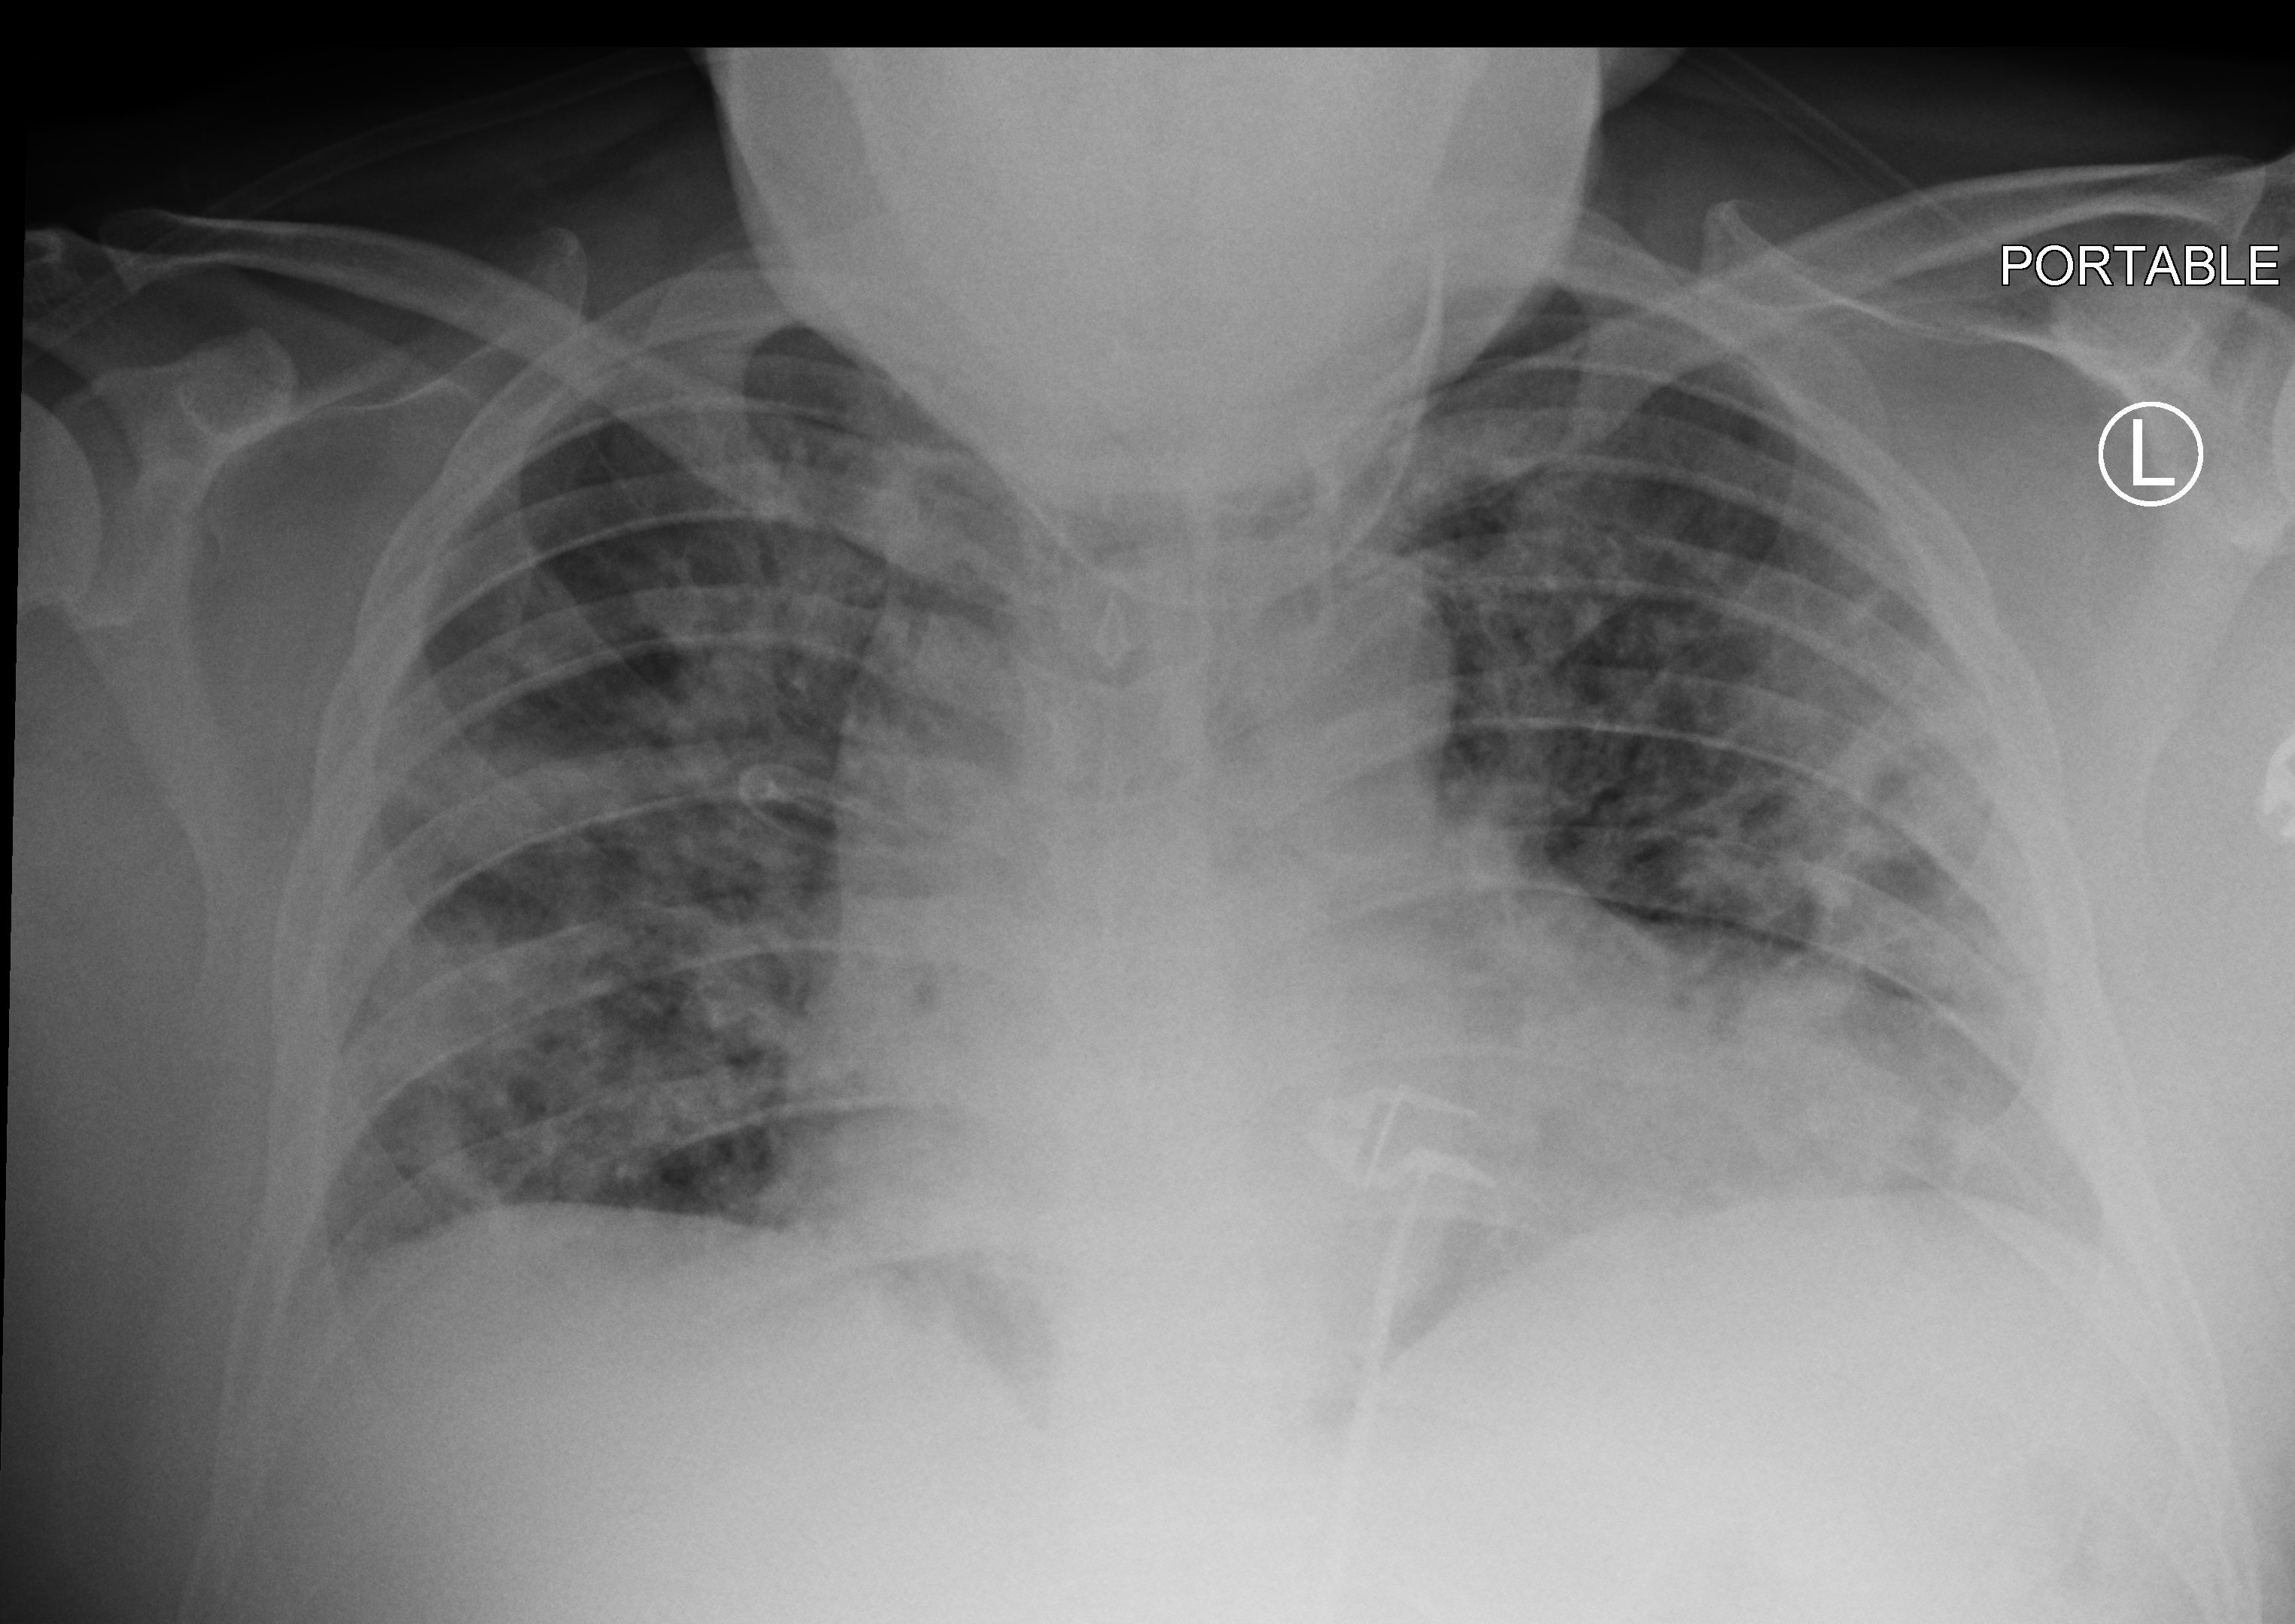
Bedside chest radiograph (computed radiography); anteroposterior (AP) projection. Male patient hospitalised with COVID-19, age 18–59 years.
Admission-level facts for this patient (not findings on this image; timing relative to this image not recorded): mechanically ventilated during this hospital stay: no; admitted to intensive care during this hospital stay: no; length of hospital stay: 20 days.